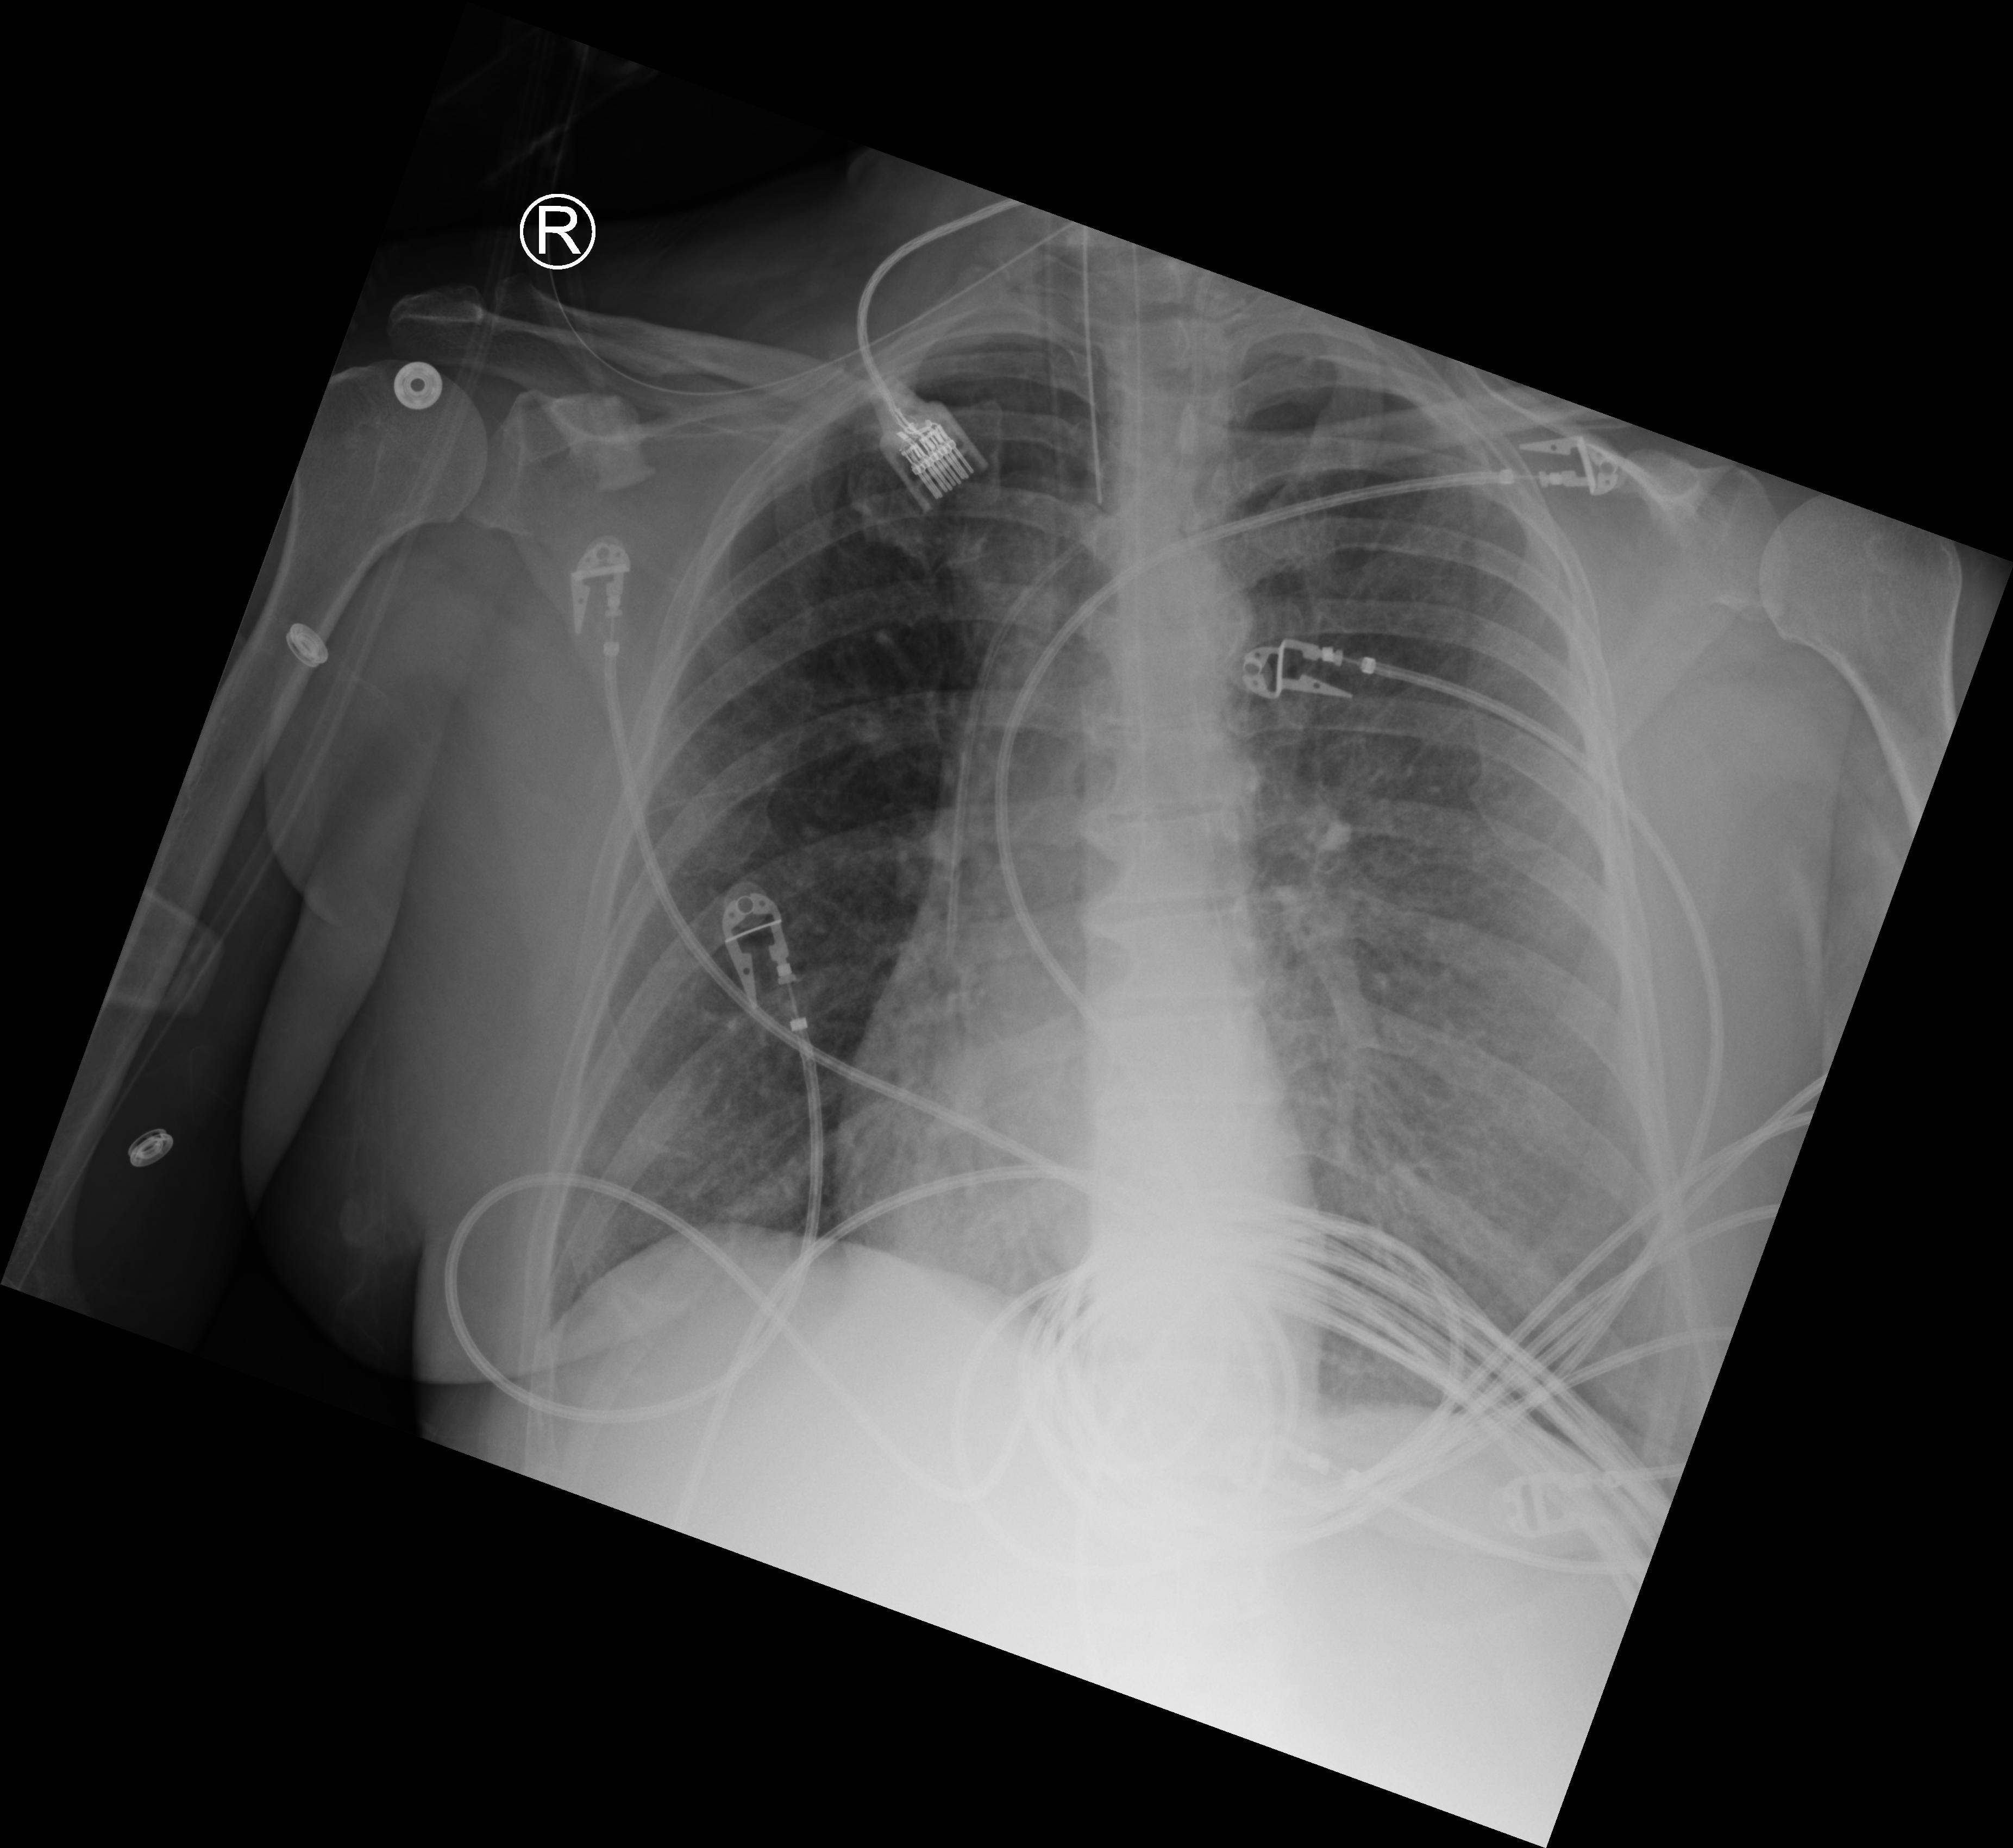
Portable chest radiograph. Patient hospitalised with COVID-19; female, aged 60–74 years.
From the hospital-stay record, not from the radiograph (when in the stay this image was taken is not recorded): hypertension (admission record): yes; admitted to intensive care during this hospital stay: yes; mechanically ventilated during this hospital stay: yes.